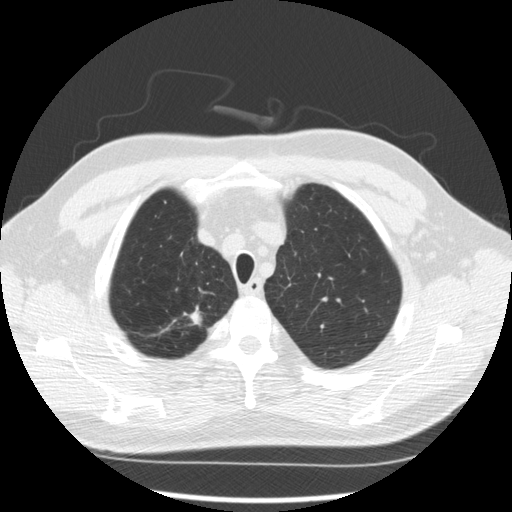
Axial slice from a low-dose chest CT screening exam; second screening round (one year after baseline); lung window (W 1500 / L -600 HU); 2.5 mm slice thickness; standard (soft-tissue) reconstruction kernel (STANDARD); 120 kVp; slice 43 of 289 in the series; 512 × 512 image matrix, field of view 360 × 360 mm. Male participant, aged 64 years at enrolment. Former smoker at enrolment.
Expert-annotated lung lesion, bounding box [x1, y1, x2, y2] px = [173, 300, 214, 336]. The screening reader recorded 3 non-calcified nodules or masses ≥4 mm on this exam (right upper lobe, right upper lobe, right upper lobe); which of them this box marks is not recorded. Lung cancer was diagnosed 411 days after this screen: adenocarcinoma, NOS, right upper lobe, moderately differentiated (G2), stage IA (AJCC 6th edition), 14 mm at pathology.